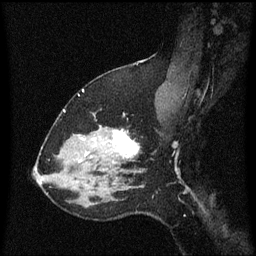
Breast MRI (dynamic contrast-enhanced), one sagittal slice; position 43 of 60 along the scan axis; dynamic contrast-enhanced series, image 2 of 3 at this slice position (ordered by acquisition); 1.5 T; TE 4.2 ms, TR 8.4 ms; 2 mm slice thickness; 256 × 256 image matrix, field of view 200 × 200 mm. Patient: female, 37 years. Case-level facts recorded for this patient, not image findings: setting: breast cancer imaged before/during neoadjuvant chemotherapy; receptor status: HR-positive, HER2-negative.
Outlined on this slice (semi-automatic segmentation, software-assisted and operator-edited):
- analysis volume of interest (the breast-tissue region the enhancement analysis was run in; not a lesion): bounding box (x1, y1, x2, y2) in pixels: (95, 114, 154, 171)
- tumour enhancement mask (voxels above the 70 % enhancement threshold inside the analysis volume of interest): (114, 130, 139, 163)